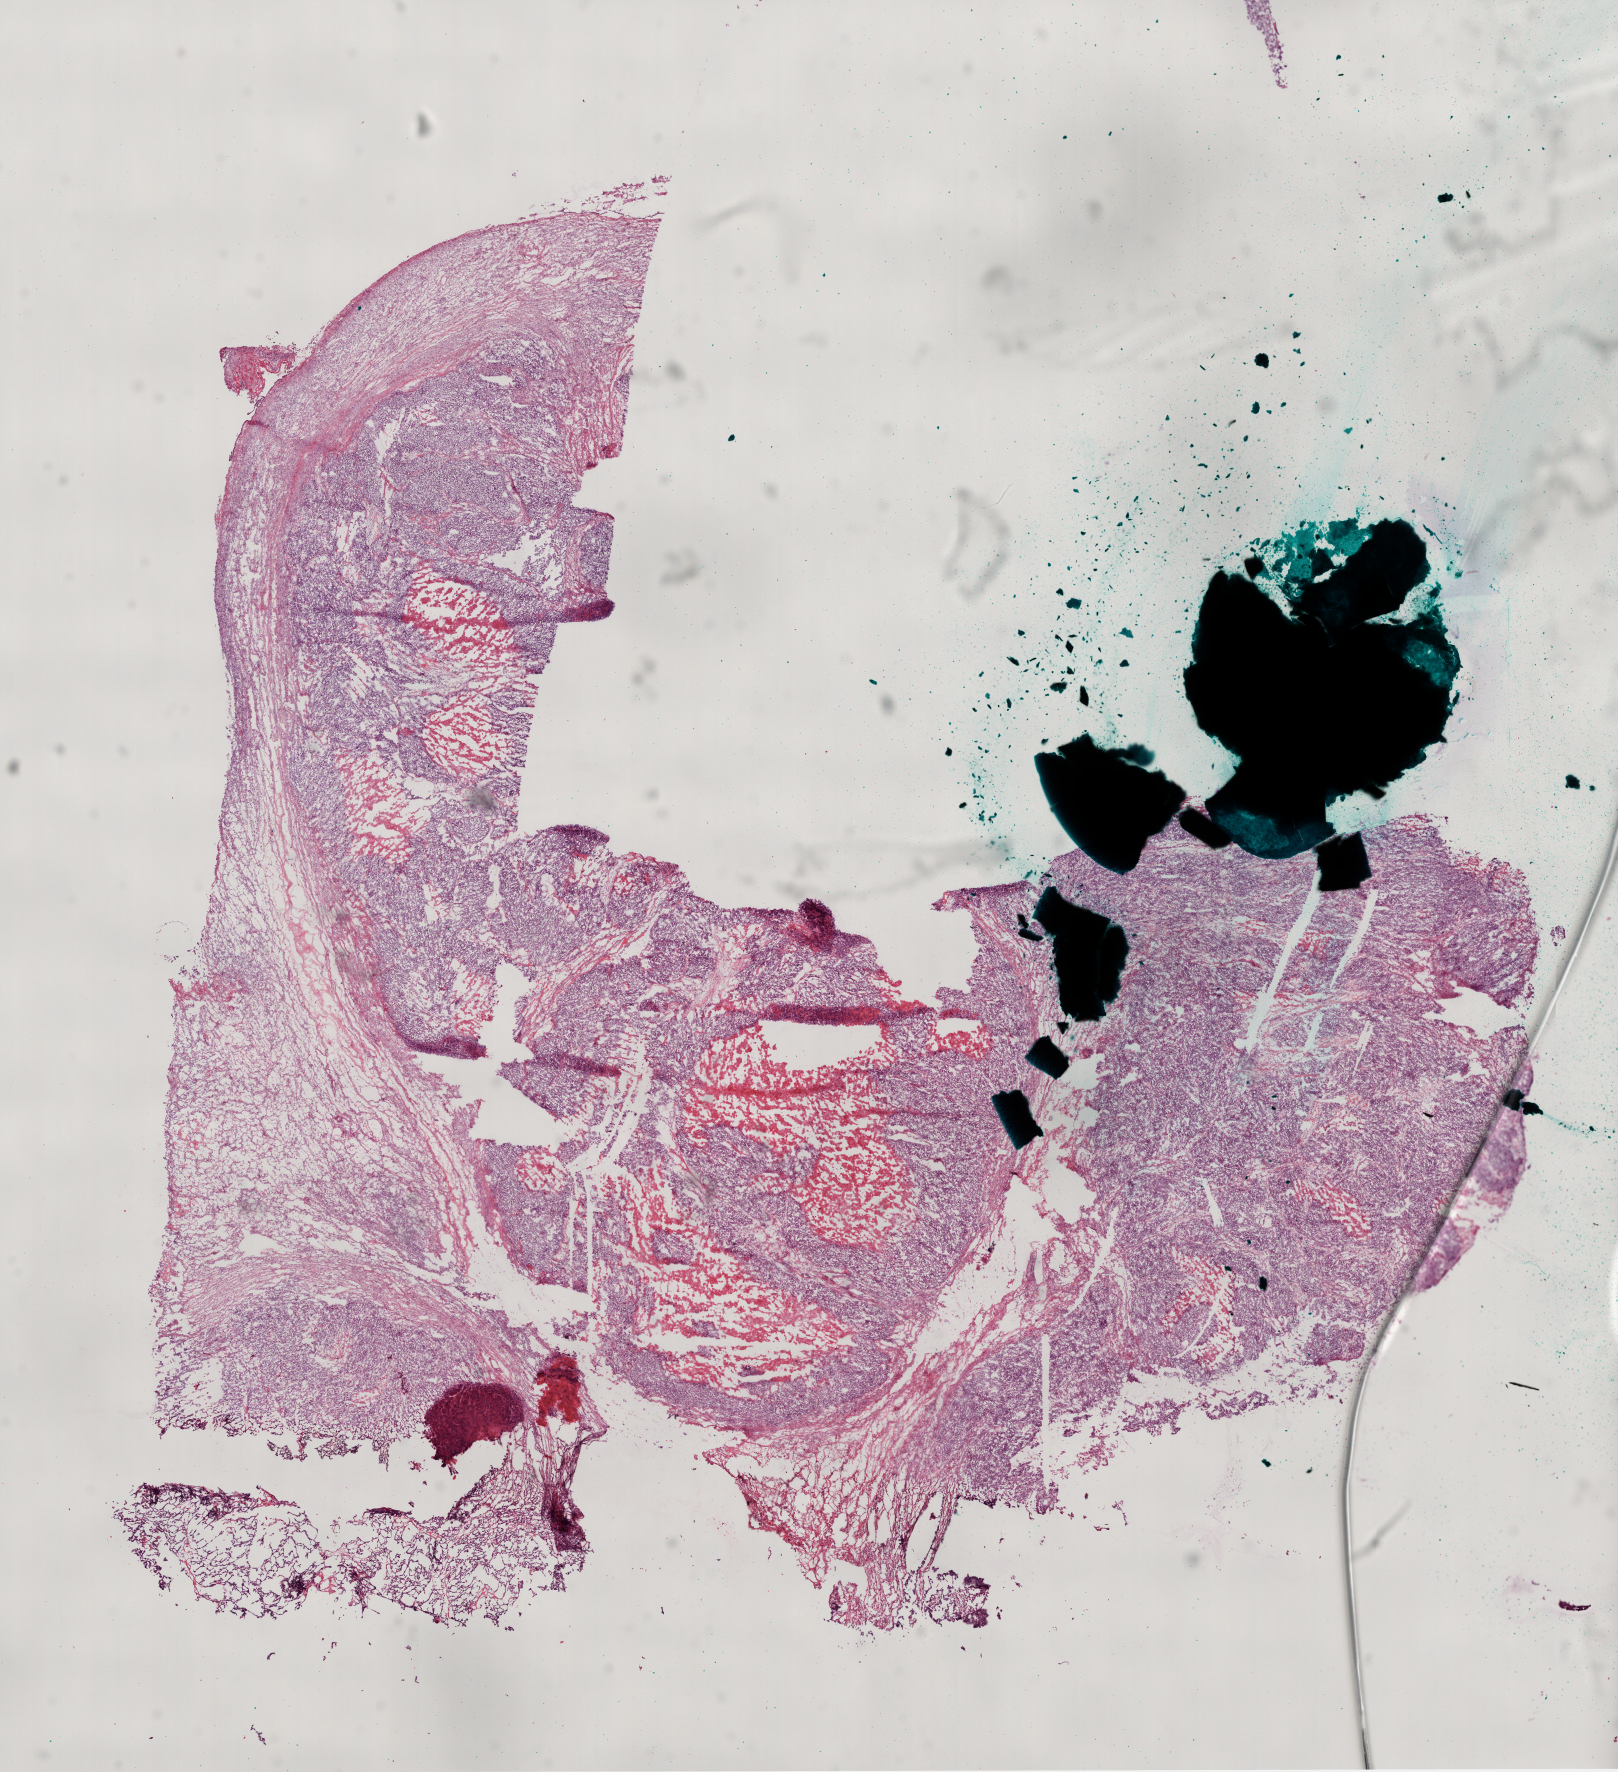
Digitized H&E-stained tissue section (whole slide) — a low-resolution overview of the entire scanned area, about 13.1 x 14.3 mm (slide scanned at 20x), frozen section, ovary, primary tumour sample. Patient: female, age at initial diagnosis 50 years. Composition of this section per pathologist review: tumour cells 60%, tumour nuclei 80%.
Pathologic diagnosis: Serous cystadenocarcinoma, NOS.